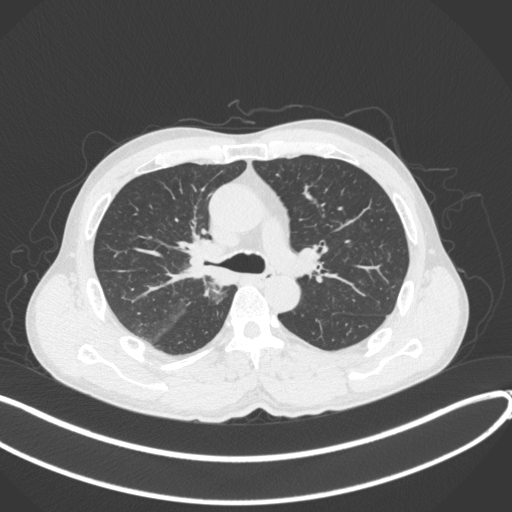
Chest CT, one axial slice. Slice 252 of 409 in the series (ordered by position). 120 kVp. Lung window (W 1500 / L -600 HU). 512 × 512 image matrix. Patient: male, 53 years. Case-level facts recorded for this patient, not image findings: clinical TNM (as recorded): T1b N0 M0.
Structures marked on this image (bounding box drawn by a radiologist):
- lung tumour (recorded histology: squamous cell carcinoma): box from (x=183, y=236) to (x=226, y=288) px